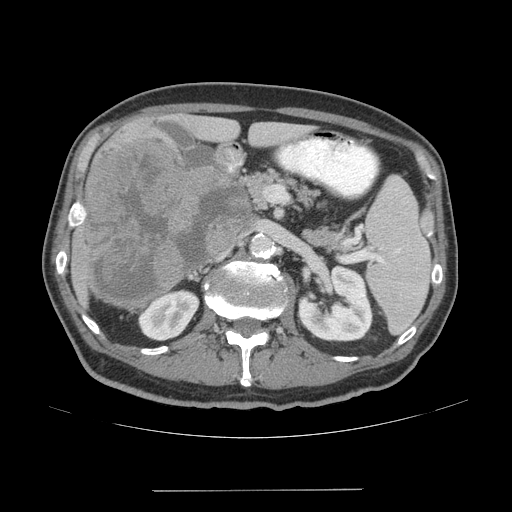
Contrast-enhanced abdominal CT (liver protocol), one axial slice. Slice 22 of 77 in the series (ordered by position). Soft-tissue window (W 400 / L 40 HU). 2.5 mm slice thickness. 512 × 512 image matrix, field of view 400 × 400 mm. Case-level facts recorded for this patient, not image findings: diagnosis: hepatocellular carcinoma (patient treated with transarterial chemoembolisation; whether this scan precedes or follows treatment is not stated here); TNM stage (as recorded): Stage-IVA; Child-Pugh class: A; tumour differentiation: well differentiated; tumour nodularity: uninodular.
Outlined on this slice (semi-automatic segmentation, software-assisted and operator-edited):
- liver parenchyma outside the tumour (the mass and vessels are separate outlines, so this box may not span the whole liver): box from (x=70, y=118) to (x=306, y=312) px
- mass: (x=83, y=138)–(x=253, y=309)